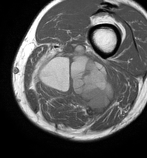
MRI of an extremity soft-tissue mass, one axial slice; position 29 of 86 along the scan axis; MR volume resampled by the dataset authors to the PET/CT grid (not the native acquisition matrix); 3.27 mm slice thickness; 147 × 158 image matrix, field of view 144 × 154 mm. Male patient. From the clinical record (not read from this slice): histological type: undifferentiated pleomorphic liposarcoma; grade: high; site of the primary tumour: left thigh.
Outlined on this slice (expert contour drawn on MRI and transferred to this co-registered scan by the dataset authors):
- gross tumour volume including surrounding oedema: bounding box [x1, y1, x2, y2] px = [30, 42, 118, 125]
- gross tumour volume (mass): [39, 58, 111, 111]